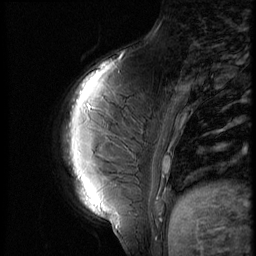
Breast MRI (dynamic contrast-enhanced), one sagittal slice. Position 15 of 56 along the scan axis. 3 images stored at this slice position (order not interpretable as contrast timing). 1.5 T. TE 4.2 ms, TR 9 ms. 256 × 256 image matrix. Patient: female, 35 years. From the clinical record (not read from this slice): setting: breast cancer imaged before/during neoadjuvant chemotherapy; receptor status: HR-positive, HER2-negative.
Annotated regions visible in this slice (semi-automatically segmented with operator editing):
- analysis volume of interest (the breast-tissue region the enhancement analysis was run in; not a lesion): bounding box [x1, y1, x2, y2] px = [60, 70, 171, 208]
- tumour enhancement mask (voxels above the 140 % enhancement threshold inside the analysis volume of interest): [166, 168, 169, 173]